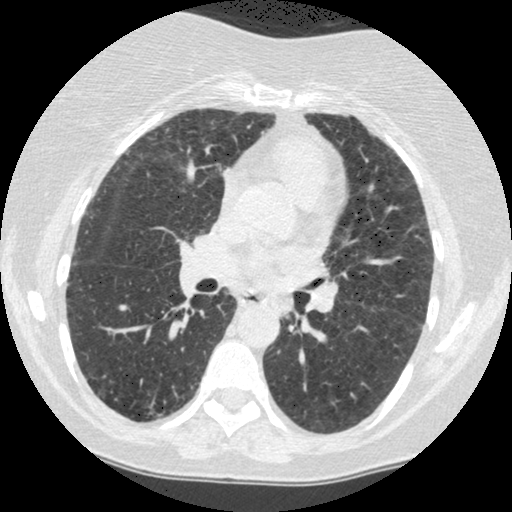
Axial slice from a low-dose chest CT screening exam; baseline annual screen; lung window (W 1500 / L -600 HU); slice 209 of 442 in the series. Female, age 60 years at enrolment. Former smoker at enrolment.
- Lesion marked by an expert reader, bounding box <265,290,307,331> (left, top, right, bottom; pixels).
- The screening reader recorded 2 non-calcified nodules or masses ≥4 mm on this exam (right lower lobe, left lower lobe); which of them this box marks is not recorded.
- Official screen result: positive, change unspecified: nodule(s) >= 4 mm or enlarging nodule(s), mass(es), or other non-specific abnormalities suspicious for lung cancer.
- Participant outcome: lung cancer diagnosed 794 days after this screen — small cell carcinoma, NOS, left lower lobe, undifferentiated (G4), stage IV (AJCC 6th edition), 69 mm at pathology.